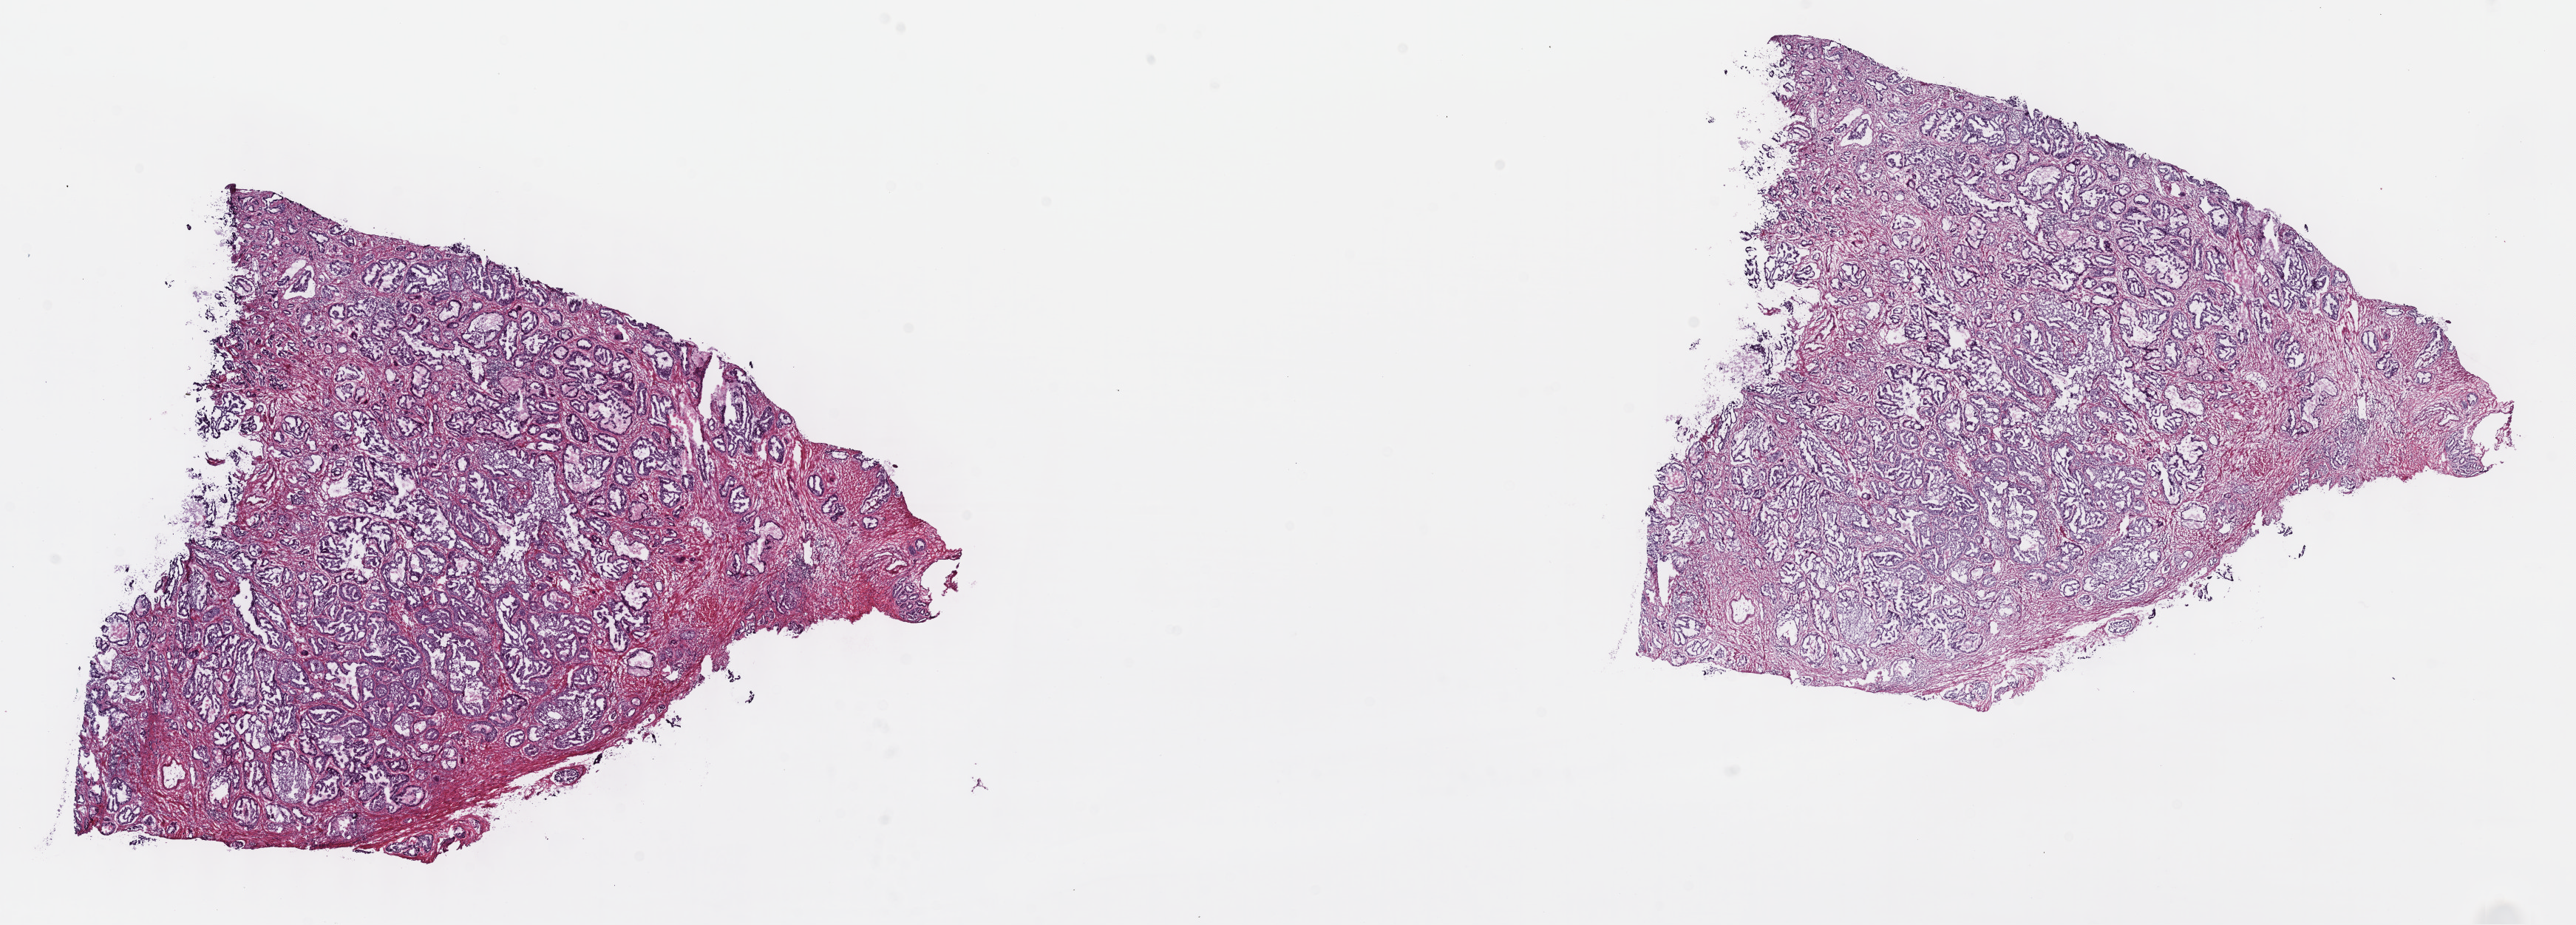
Hematoxylin and eosin (H&E) stained whole-slide image, a low-resolution overview of the entire scanned area, about 28.2 x 10.1 mm (slide scanned at 40x), frozen section from the top of the tissue portion, sample: primary tumour, prostate. Male, age 50 years at initial diagnosis. Gleason score: 7 (4+3). Pathologist review of this section (percent, as recorded): tumour cells 40%, tumour nuclei 60%, normal cells 30%, stromal cells 30%, necrosis 0%. Inflammatory infiltration, as recorded: lymphocyte infiltration 0%, monocyte infiltration 0%, neutrophil infiltration 0%.
- diagnosis: Adenocarcinoma, NOS (prostate gland)